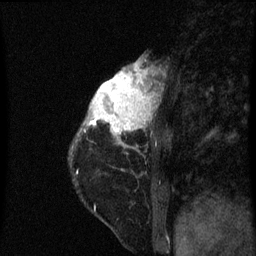
Breast MRI (dynamic contrast-enhanced), one sagittal slice; slice 18 of 60 in the series (ordered by position); dynamic contrast-enhanced series, image 2 of 3 at this slice position (ordered by acquisition); 1.5 T; TE 4.2 ms, TR 8 ms; 2 mm slice thickness; 256 × 256 image matrix. Patient: female, 38 years.
Structures marked on this image (semi-automatic segmentation, software-assisted and operator-edited):
- analysis volume of interest (the breast-tissue region the enhancement analysis was run in; not a lesion): bounding box <80,64,163,151> (left, top, right, bottom; pixels)
- tumour enhancement mask (voxels above the 70 % enhancement threshold inside the analysis volume of interest): <84,64,153,139>